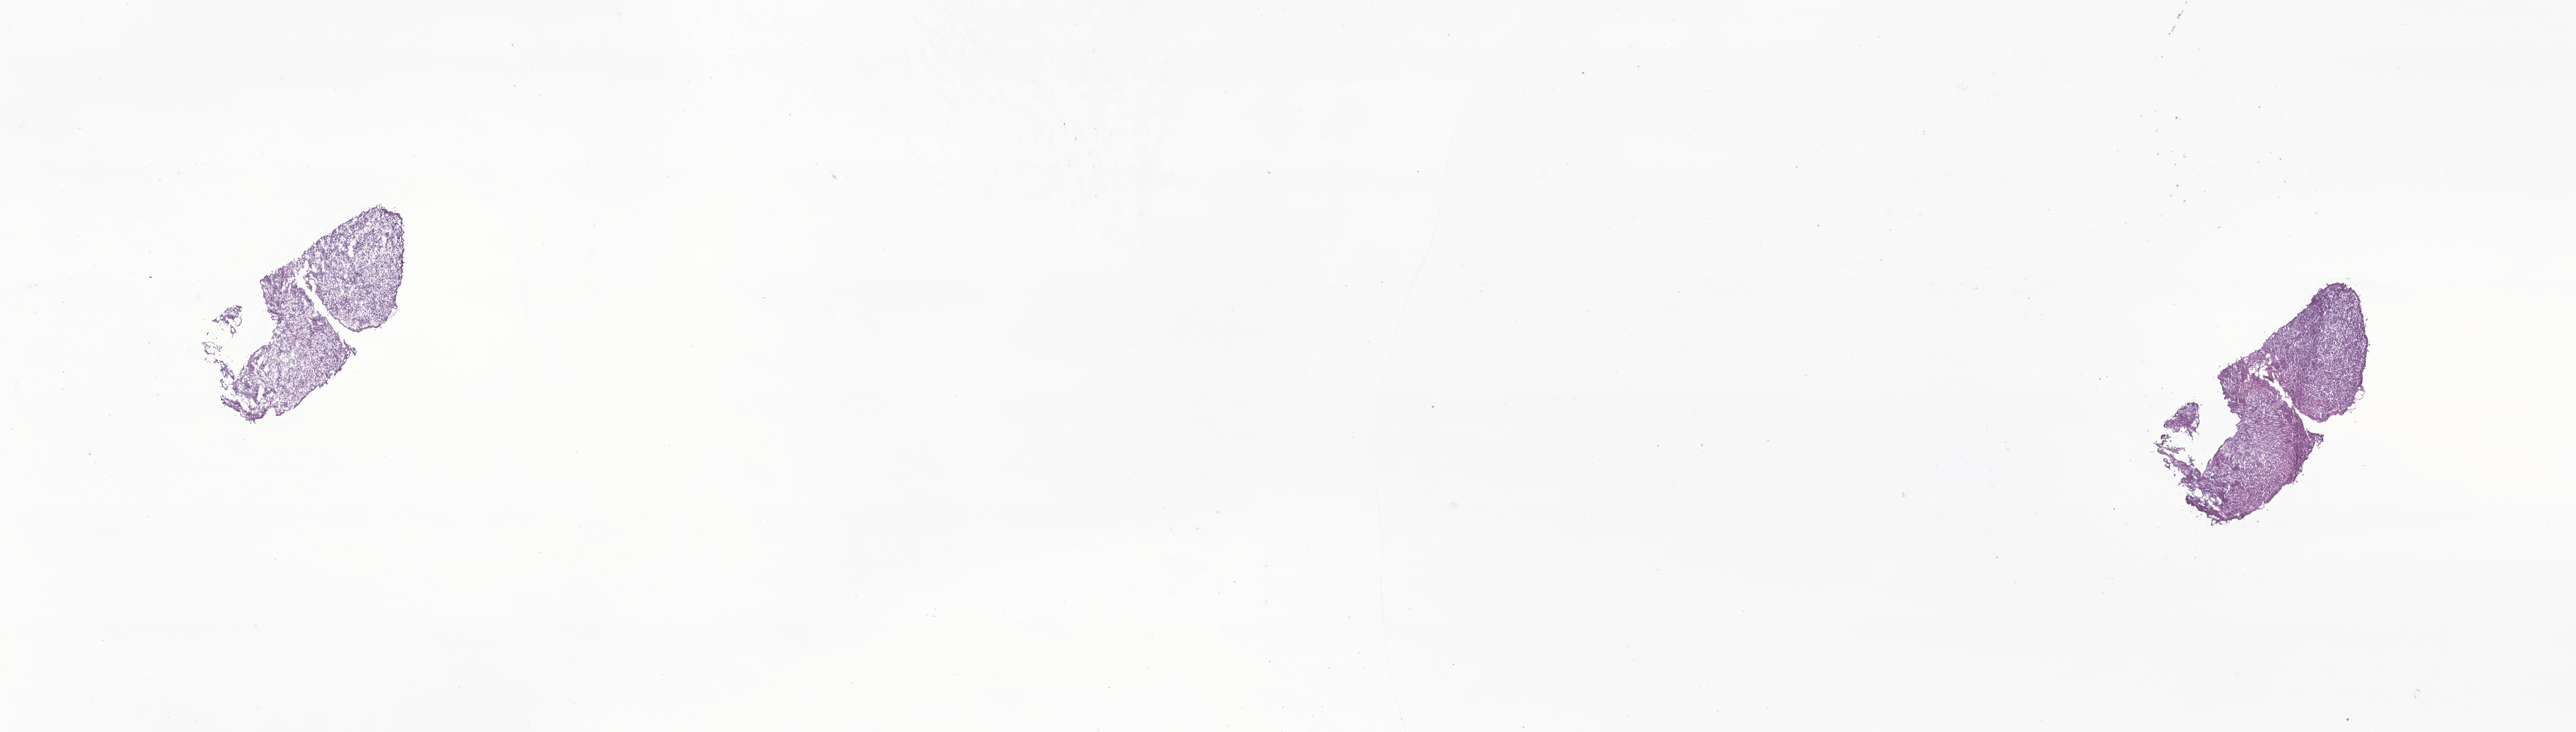
Digitized hematoxylin and eosin (H&E)-stained section of tumor tissue from the brain stem, low-resolution overview of the scanned area, about 24.2 x 6.9 mm, cryosection (OCT / tissue freezing medium). Male patient, age 71 months (5 years 11 months).
• diagnosis: Glioma, malignant